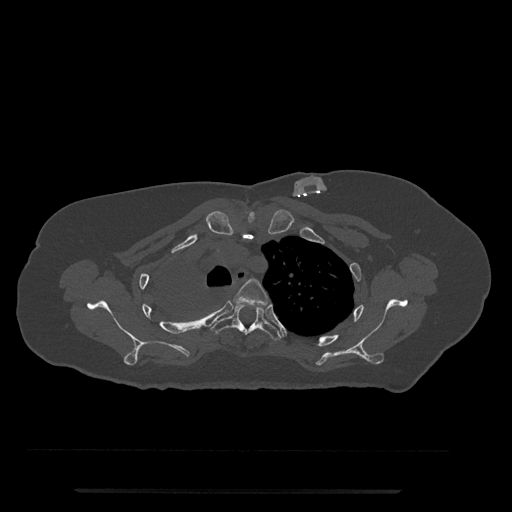
CT including the spine, one axial slice; position 605 of 797 along the scan axis; 120 kVp; bone window (W 1800 / L 400 HU); 0.5 mm slice thickness; 512 × 512 image matrix. Patient: female, 51 years. From the clinical record (not read from this slice): primary cancer: neuro; vertebrae with lytic lesions (as recorded): T8.
Outlined on this slice (semi-automatic segmentation, software-assisted and operator-edited):
- T3 vertebra: bounding box <234,278,269,306> (left, top, right, bottom; pixels)
- T4 vertebra: <210,304,282,341>